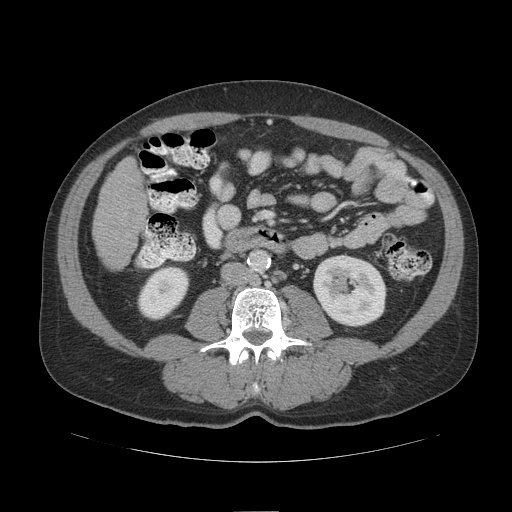
Contrast-enhanced abdominal CT (liver protocol), one axial slice; slice 29 of 109 in the series (ordered by position); soft-tissue window (W 400 / L 40 HU); 2.5 mm slice thickness; 512 × 512 image matrix, field of view 420 × 420 mm. Case-level facts recorded for this patient, not image findings: diagnosis: hepatocellular carcinoma (patient treated with transarterial chemoembolisation; whether this scan precedes or follows treatment is not stated here); TNM stage (as recorded): Stage-IIIB; Child-Pugh class: A; tumour differentiation: poorly differentiated; tumour nodularity: multinodular.
Annotated regions visible in this slice (semi-automatic segmentation, software-assisted and operator-edited):
- liver parenchyma outside the tumour (the mass and vessels are separate outlines, so this box may not span the whole liver): box from (x=94, y=156) to (x=146, y=268) px